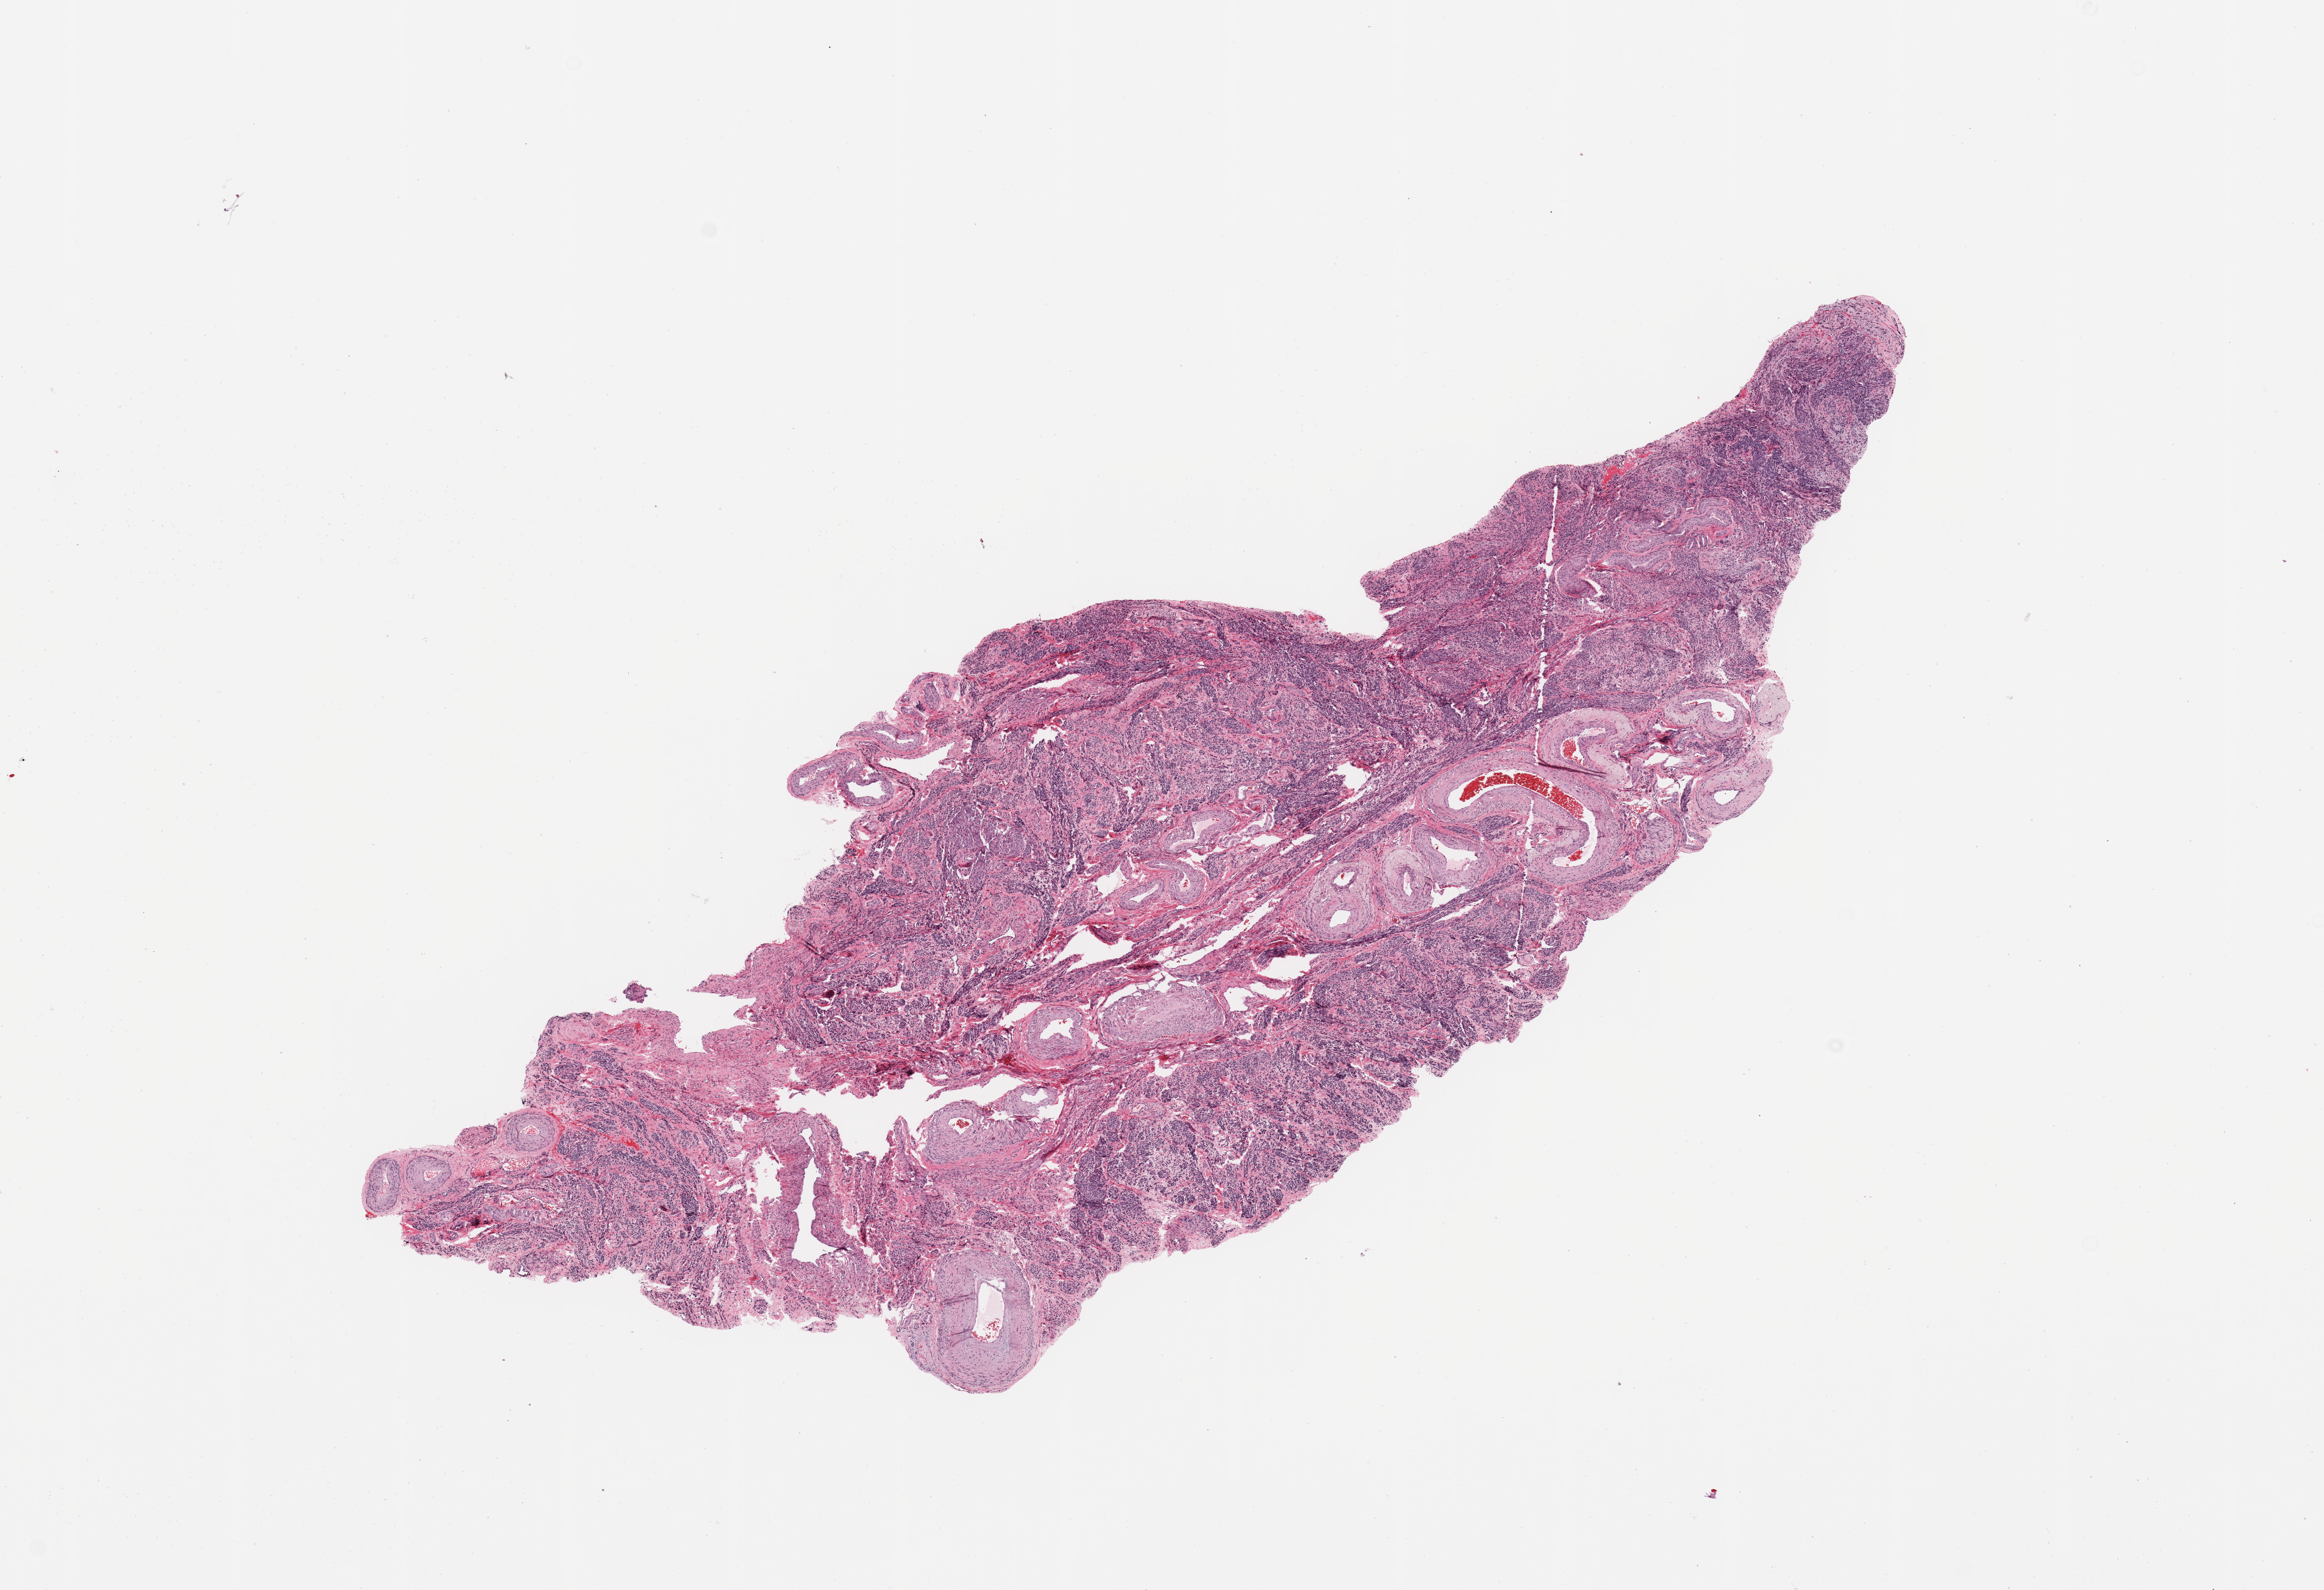
Whole-slide histology image, H&E, low-resolution overview of the scanned area, about 13.8 x 9.4 mm (slide scanned at 20x). Patient: female, age 60 years.
Patient diagnosis (cohort enrolment): sarcoma (site not recorded at cohort level).